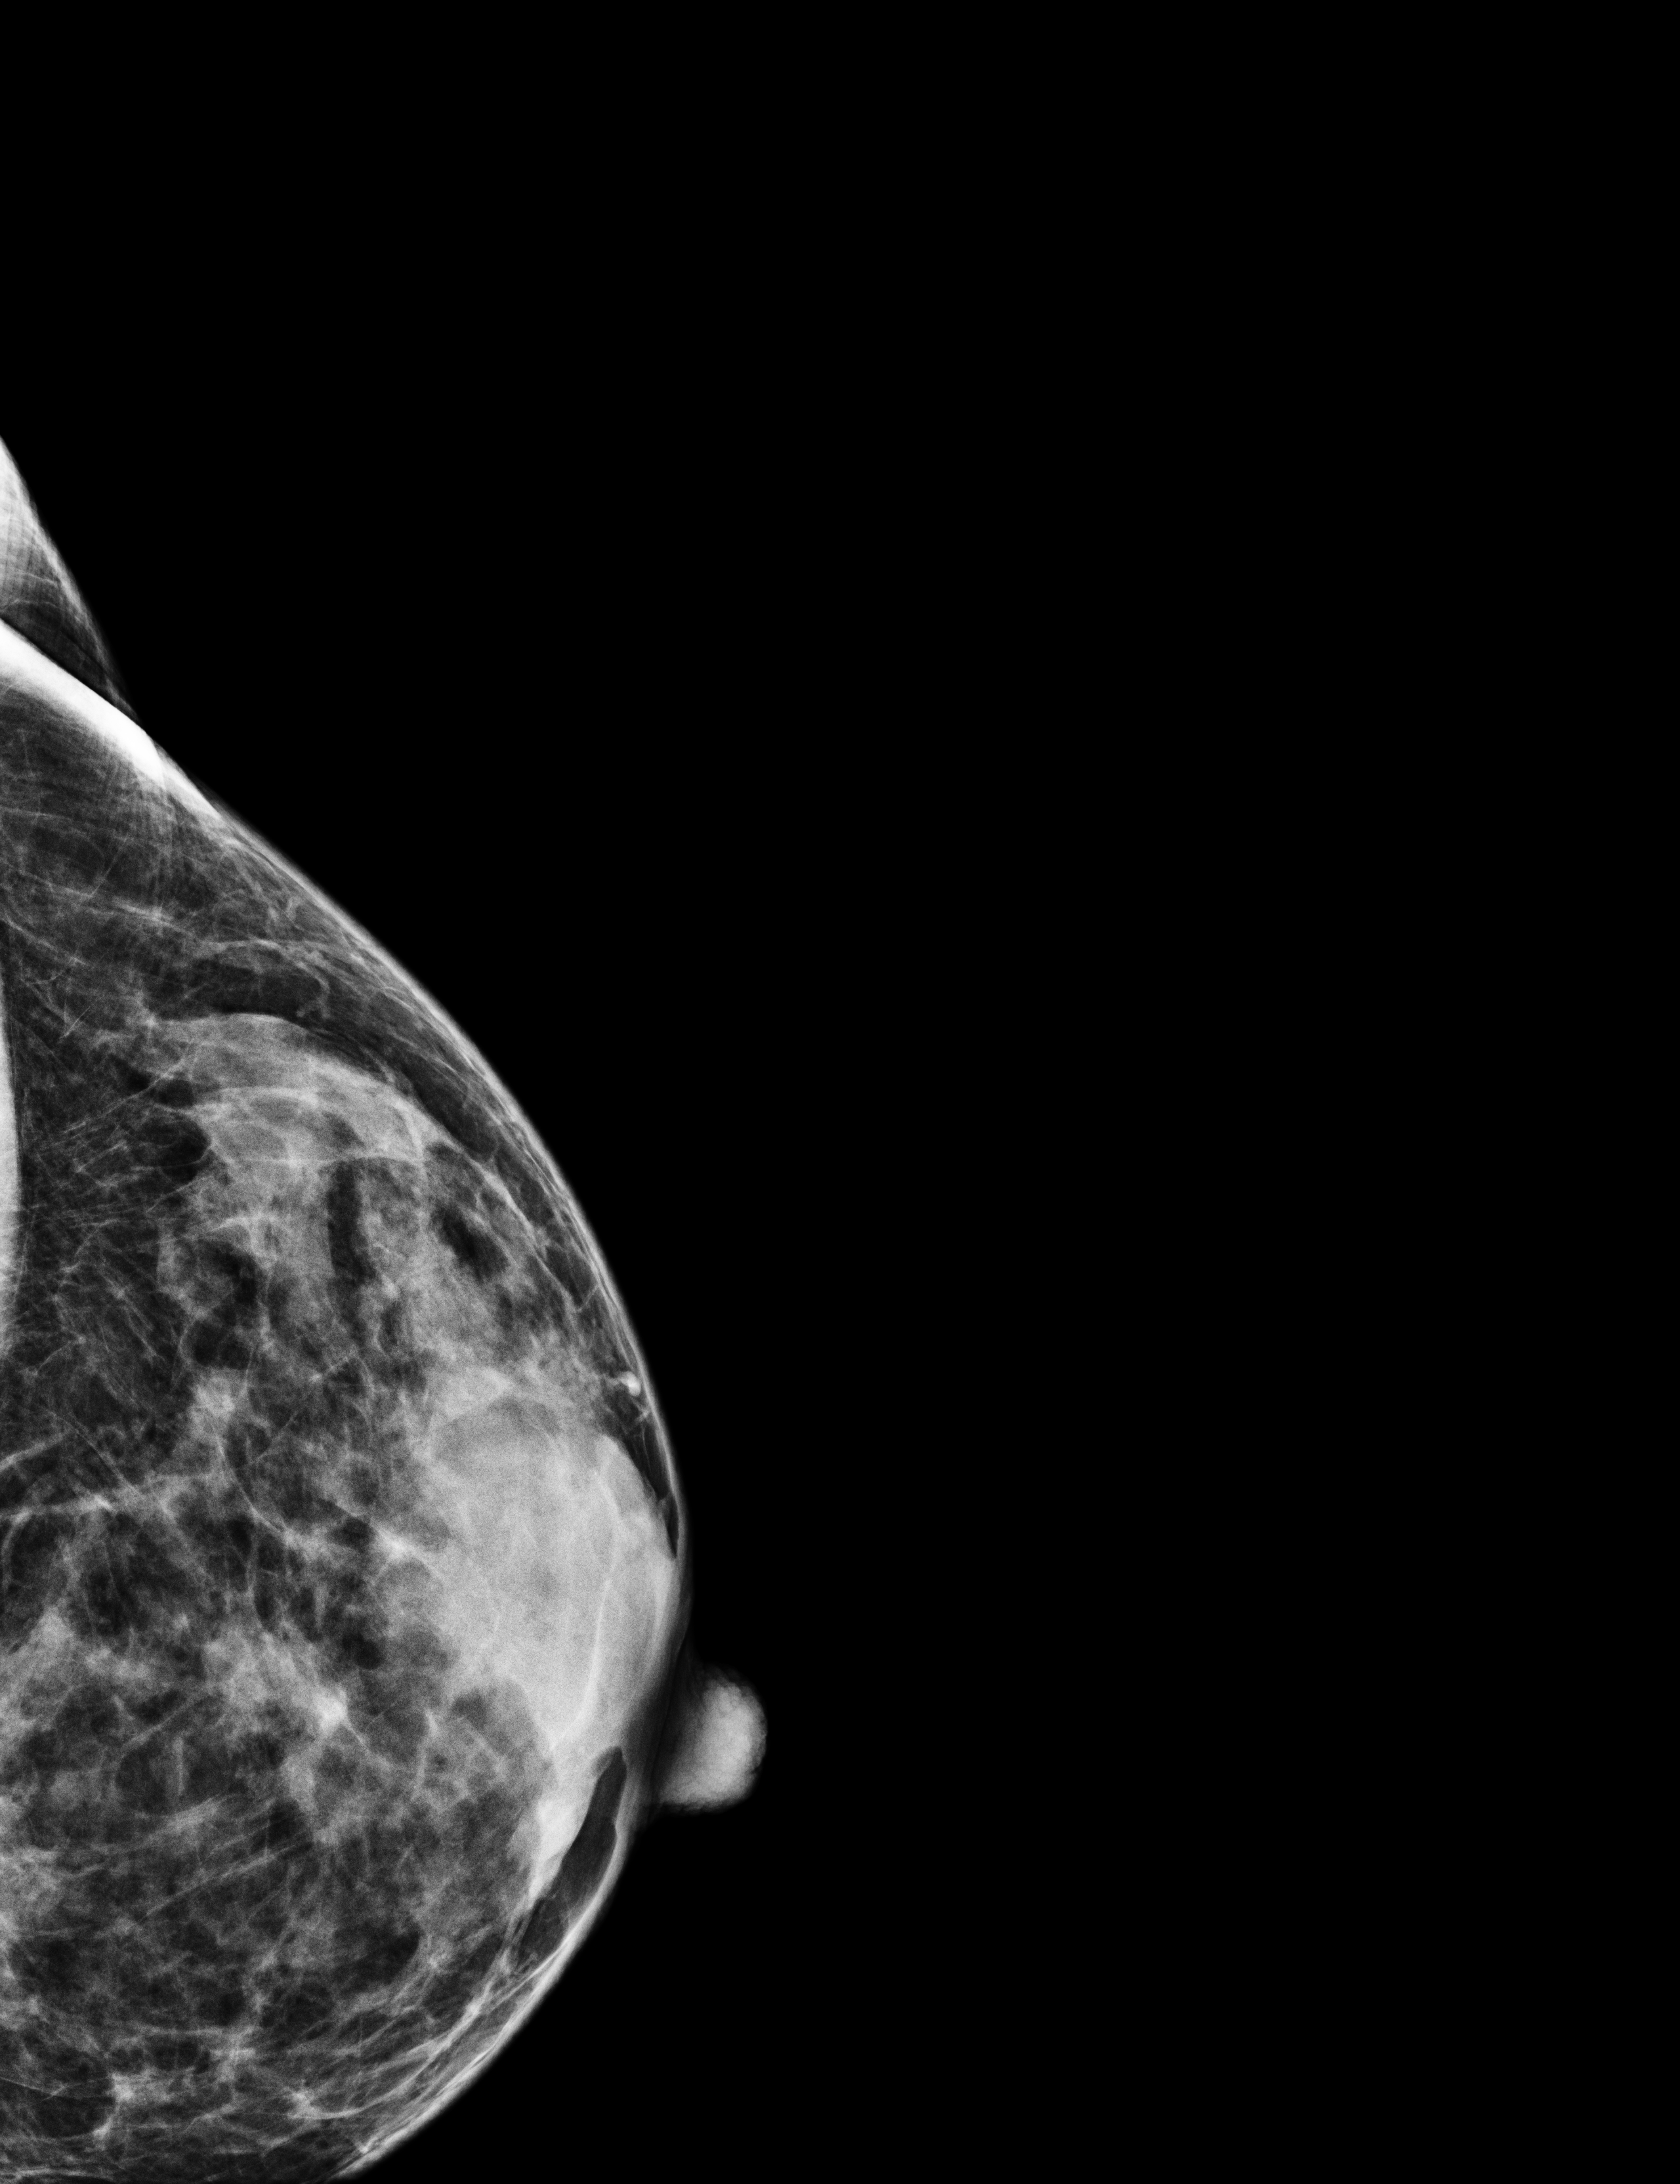
Annual screening mammography examination. Patient aged 50 years (female).
Image type: full-field digital mammogram. Breast: left. Projection: laterally exaggerated craniocaudal (XCCL) view.